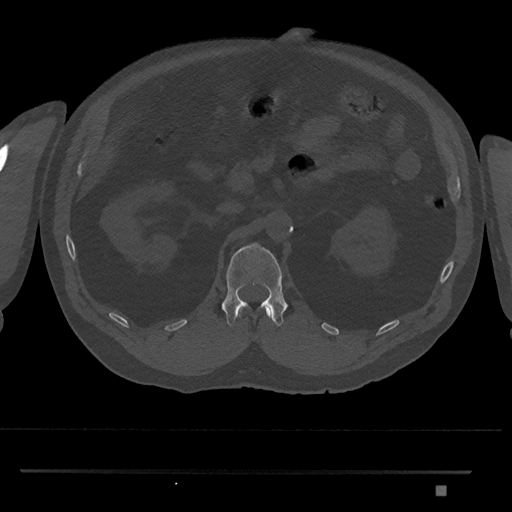
CT including the spine, one axial slice; 120 kVp; bone window (W 1800 / L 400 HU); 512 × 512 image matrix. Male patient, age 65 years. From the clinical record (not read from this slice): primary cancer: prostate.
Annotated regions visible in this slice (semi-automatic segmentation, software-assisted and operator-edited):
- L1 vertebra: box from (x=222, y=243) to (x=288, y=327) px
- T12 vertebra: (x=237, y=308)–(x=272, y=318)